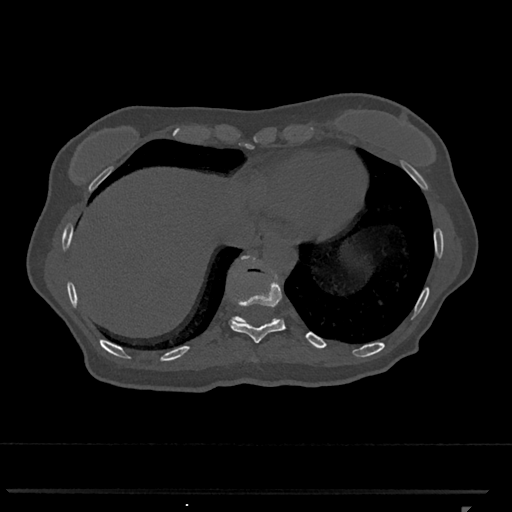
CT including the spine, one axial slice. Bone window (W 1800 / L 400 HU). 512 × 512 image matrix, field of view 380 × 380 mm. Female patient, age 62 years. Case-level facts recorded for this patient, not image findings: primary cancer: renal.
Outlined on this slice (semi-automatically segmented with operator editing):
- T10 vertebra: bounding box [x1, y1, x2, y2] px = [229, 266, 285, 343]
- T11 vertebra: [232, 255, 277, 324]